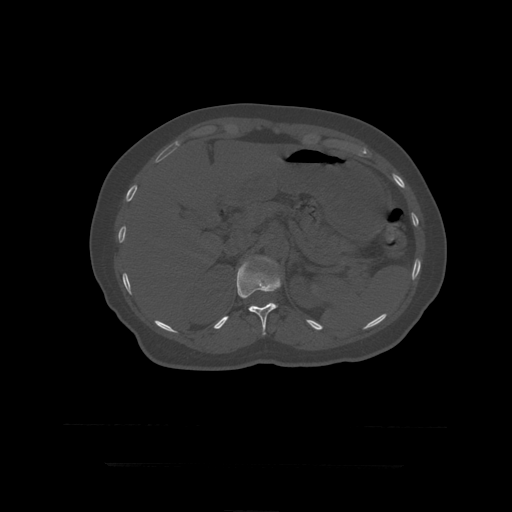
CT including the spine, one axial slice; position 193 of 399 along the scan axis; reconstruction kernel STANDARD; 120 kVp; bone window (W 1800 / L 400 HU); 1.25 mm slice thickness; 512 × 512 image matrix, field of view 450 × 450 mm. Patient age 41 years. From the clinical record (not read from this slice): primary cancer: breast.
Outlined on this slice (semi-automatically segmented with operator editing):
- L1 vertebra: box from (x=254, y=257) to (x=277, y=266) px
- T12 vertebra: (x=237, y=260)–(x=281, y=335)